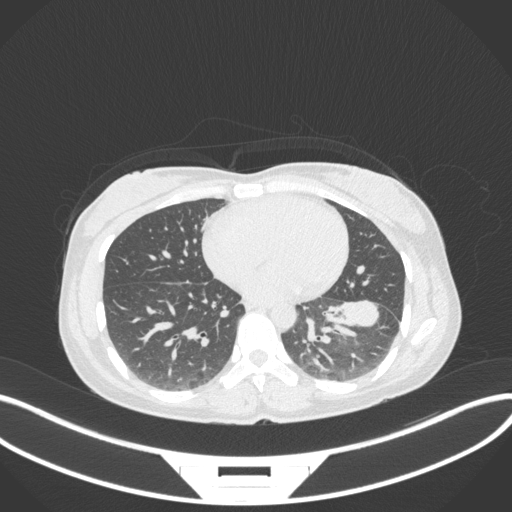
Chest CT, one axial slice. Slice 145 of 361 in the series (ordered by position). Lung window (W 1500 / L -600 HU). 1 mm slice thickness. 512 × 512 image matrix. Female patient, age 41 years. From the clinical record (not read from this slice): clinical TNM (as recorded): T2a N3 M1b.
Outlined on this slice (rectangle marked by the reading radiologist):
- lung tumour (recorded histology: adenocarcinoma): bounding box (x1, y1, x2, y2) in pixels: (323, 292, 389, 333)